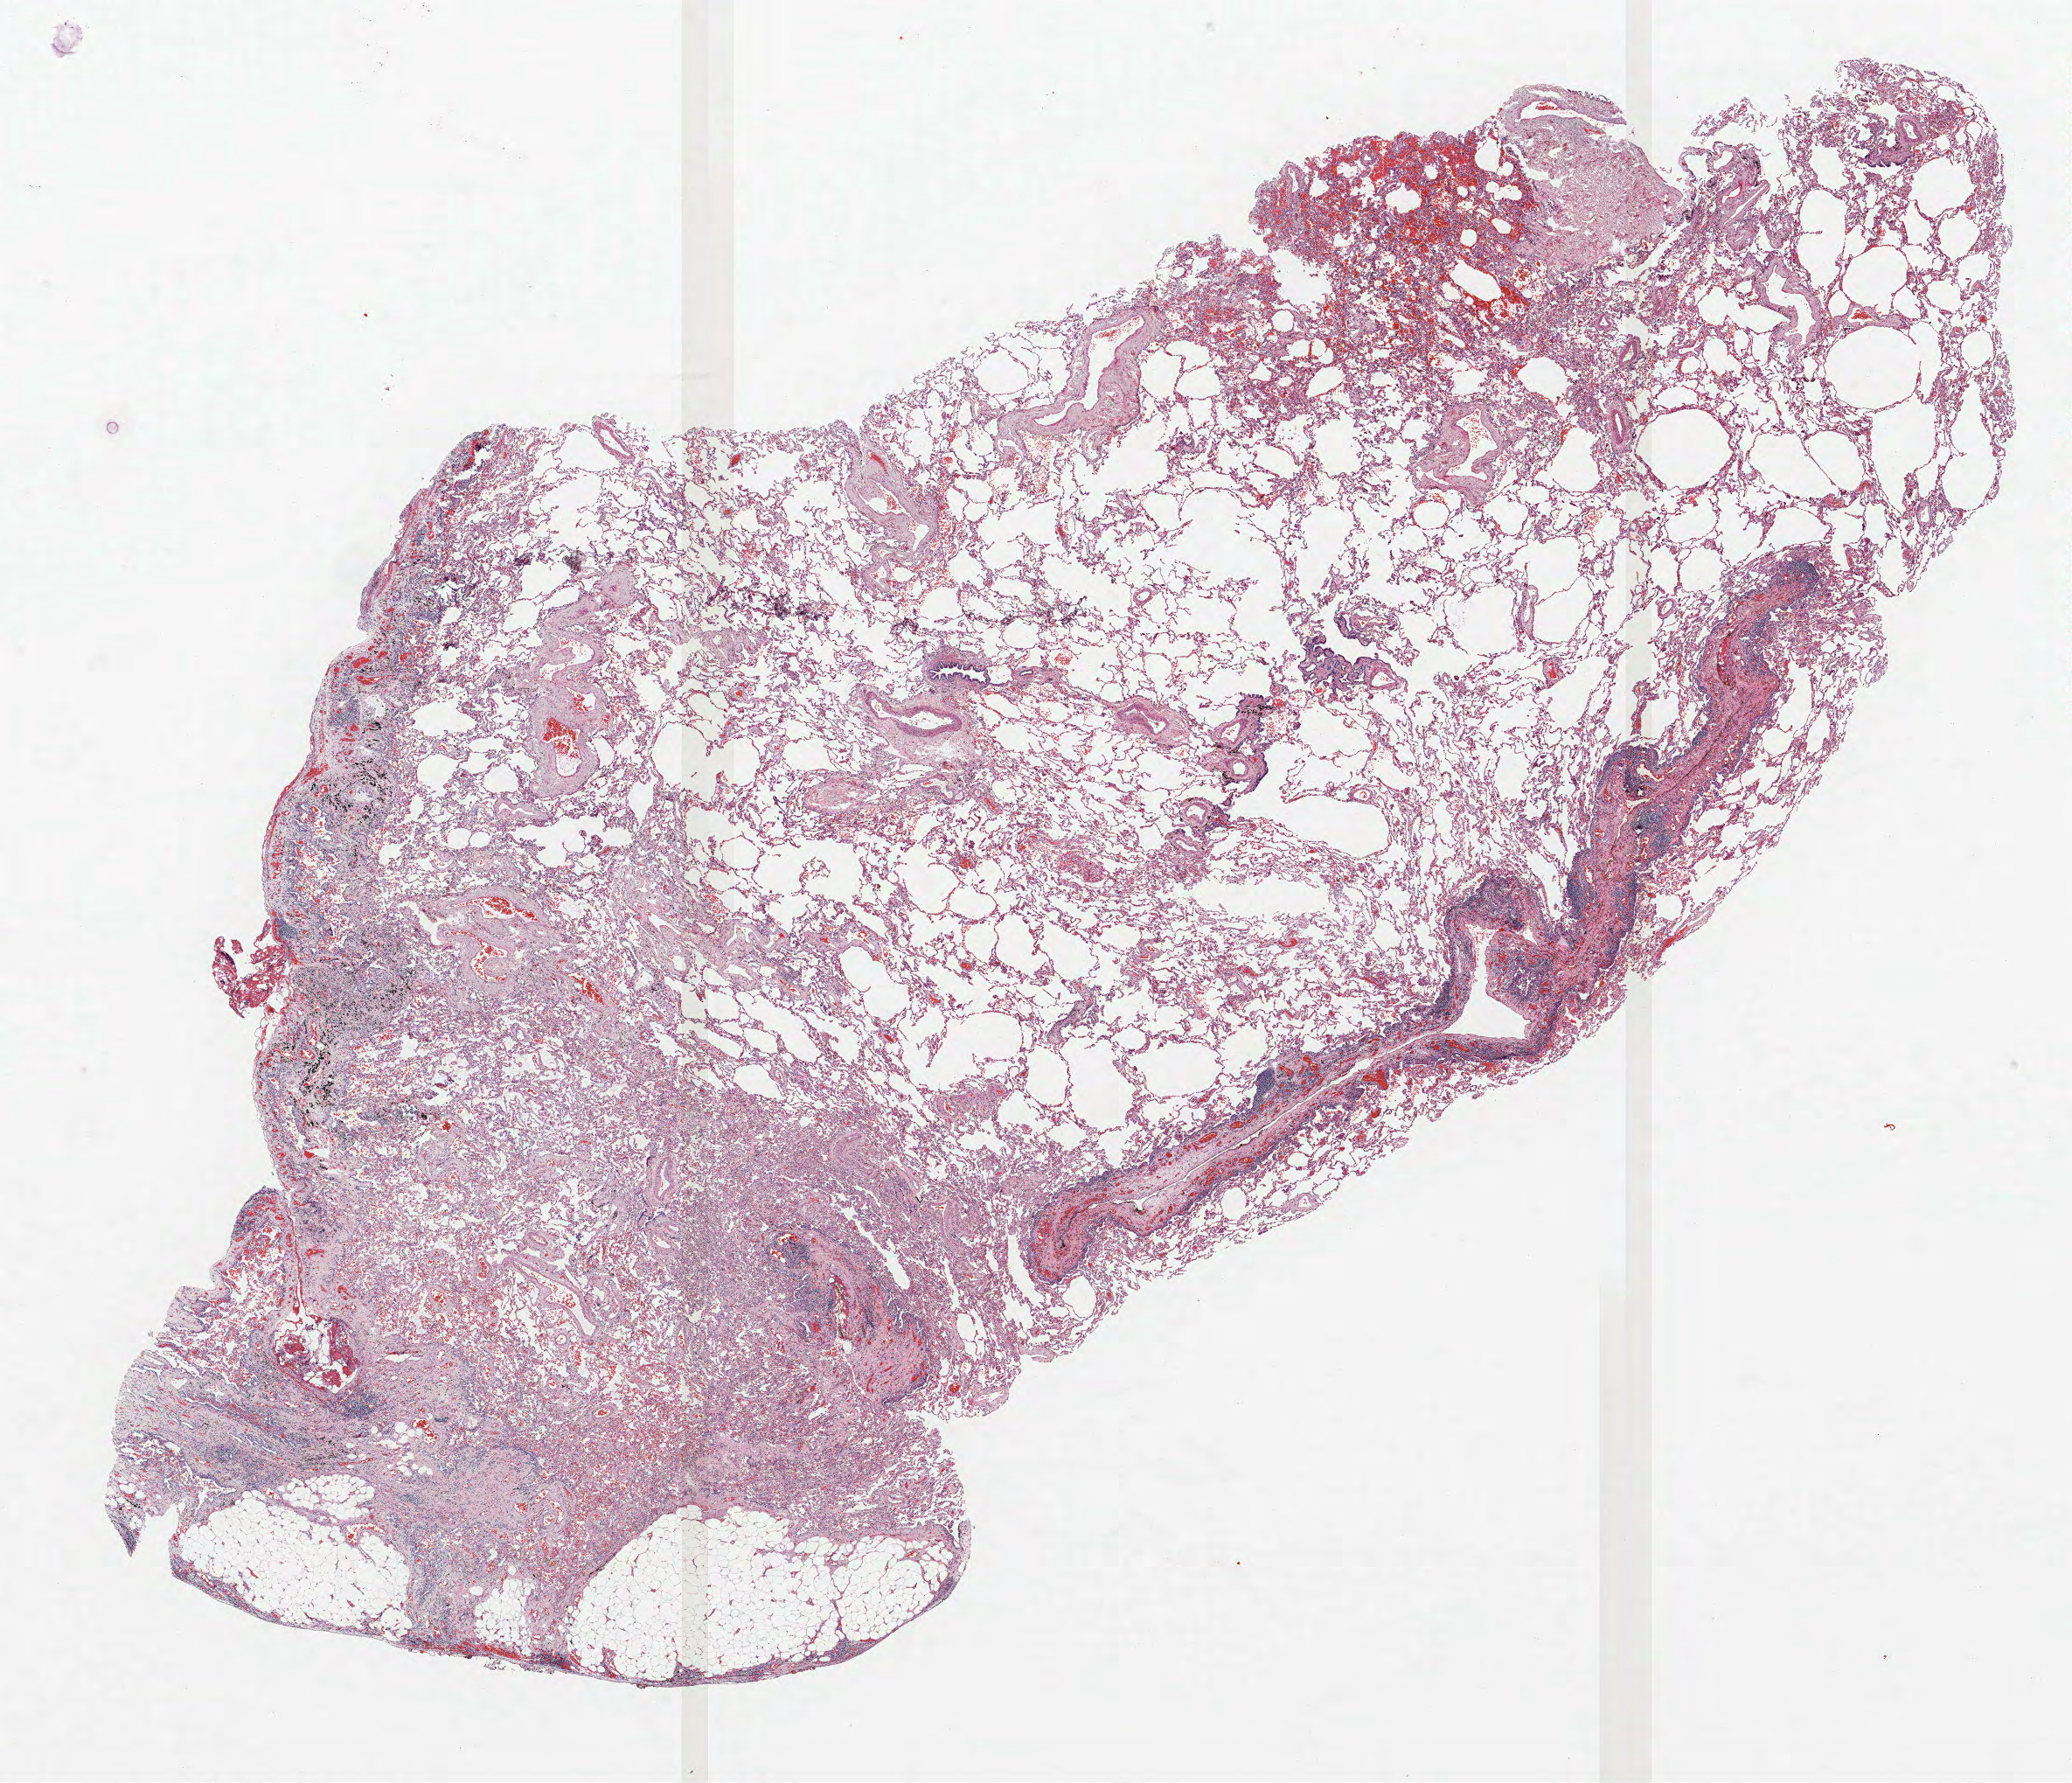
Whole-slide histology image, Hematoxylin and eosin (H&E) stained — low-resolution overview of the scanned area, about 19.0 x 16.3 mm; formalin-fixed paraffin-embedded (FFPE) section; lung tissue. Male, age 62 at enrolment. Grade: poorly differentiated (G3).
- tumour size (pathology): 15 mm
- primary tumour location (clinical record): right lower lobe
- stage (AJCC 6th edition): IV
- participant's lung-cancer diagnosis: Adenocarcinoma, NOS (ICD-O-3 8140/3)